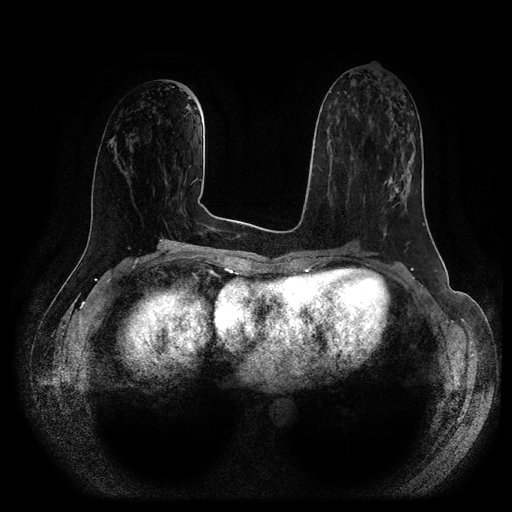
Breast MRI (dynamic contrast-enhanced, multi-phase), one axial slice; slice 46 of 116 in the series (ordered by position); dynamic contrast-enhanced series, time point 2 of 5 at this slice position (early post-contrast); 1.5 T; TE 2.6 ms, TR 5.2 ms; 2 mm slice thickness; 512 × 512 image matrix, field of view 380 × 380 mm. Patient: female, 57 years.
Structures marked on this image (semi-automatically segmented with operator editing):
- breast lesion (labelled 'tumour' in the annotation; benign lesions carry a separate 'benign' label): bounding box [x1, y1, x2, y2] px = [384, 152, 415, 197]